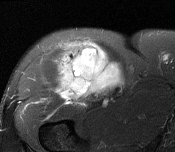
MRI of an extremity soft-tissue mass, one axial slice; slice 106 of 116 in the series (ordered by position); T2-weighted fat-saturated; MR volume resampled by the dataset authors to the PET/CT grid (not the native acquisition matrix); 175 × 152 image matrix, field of view 171 × 148 mm. Male patient. From the clinical record (not read from this slice): histological type: pleiomorphic leiomyosarcoma; grade: intermediate; site of the primary tumour: right thigh.
Outlined on this slice (expert contour drawn on MRI and transferred to this co-registered scan by the dataset authors):
- gross tumour volume including surrounding oedema: bounding box (x1, y1, x2, y2) in pixels: (56, 42, 121, 100)
- gross tumour volume (mass): (58, 49, 119, 98)